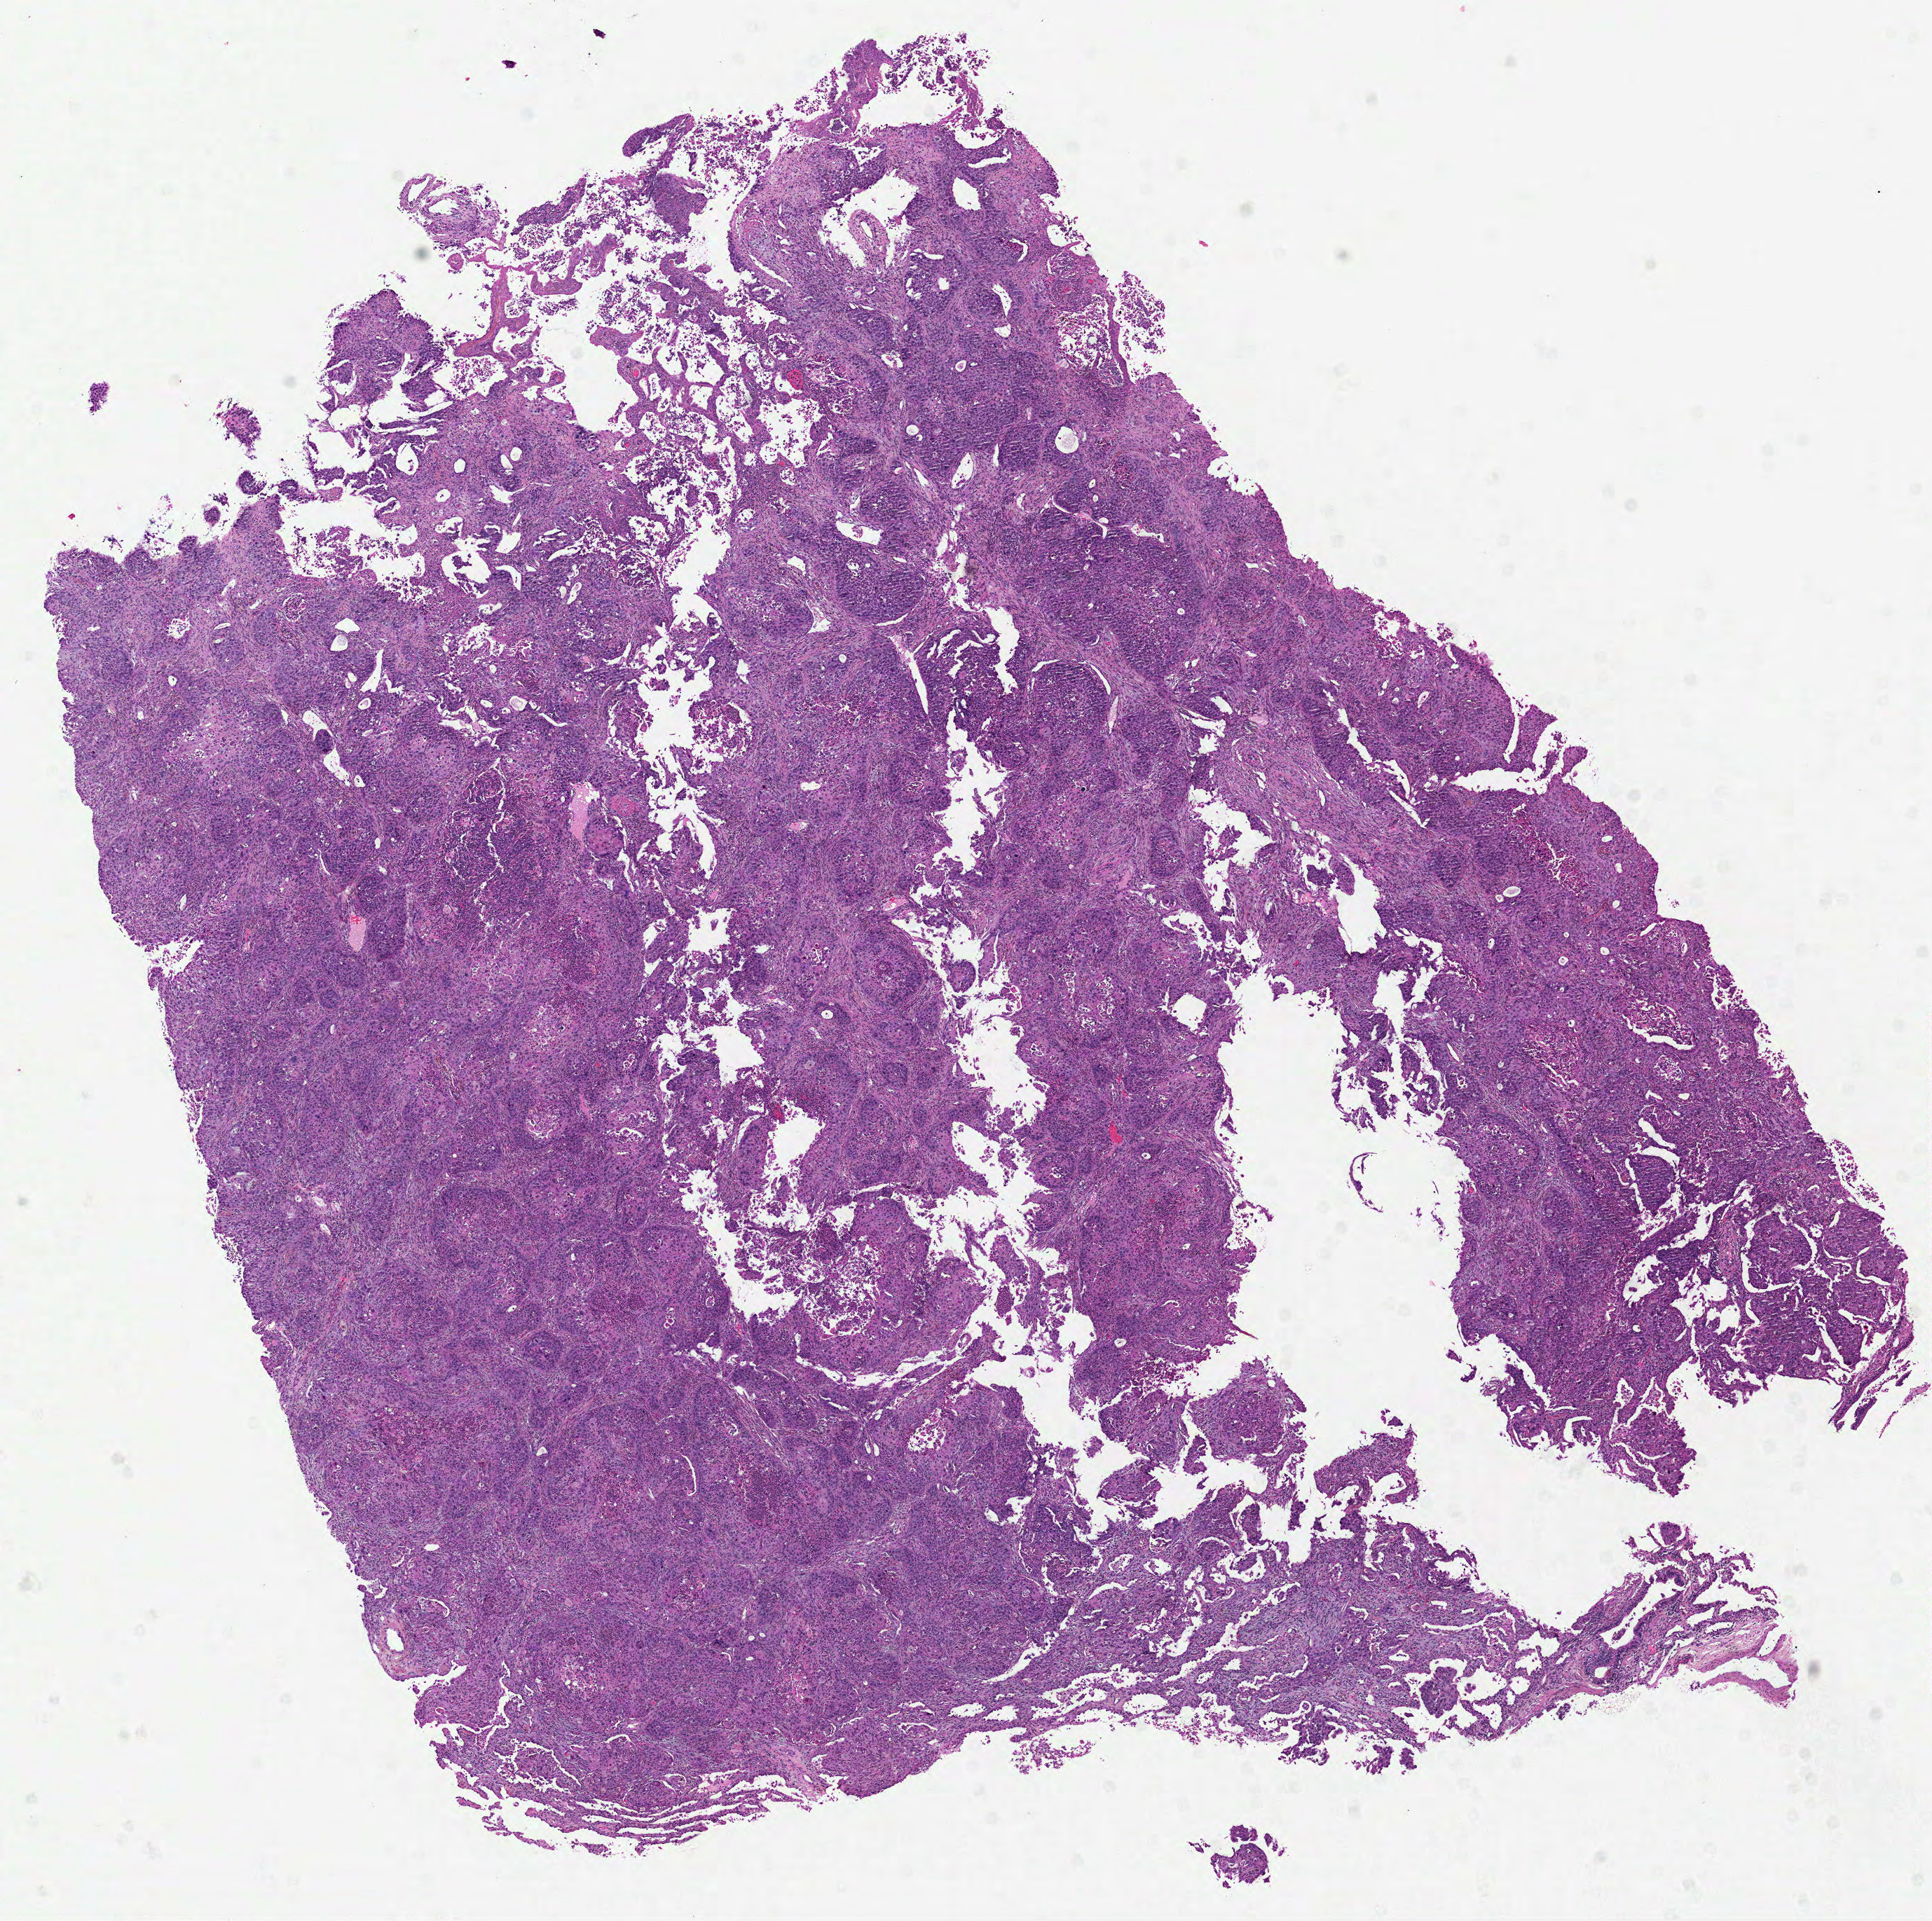
H&E-stained whole-slide image, low-resolution overview of the scanned area, about 11.1 x 11.1 mm, formalin-fixed paraffin-embedded (FFPE) diagnostic section, lung, primary tumour sample. Patient: female, age at initial diagnosis 62 years.
AJCC pathologic stage: IB. Pathologic diagnosis: Squamous cell carcinoma, NOS (lower lobe, lung).